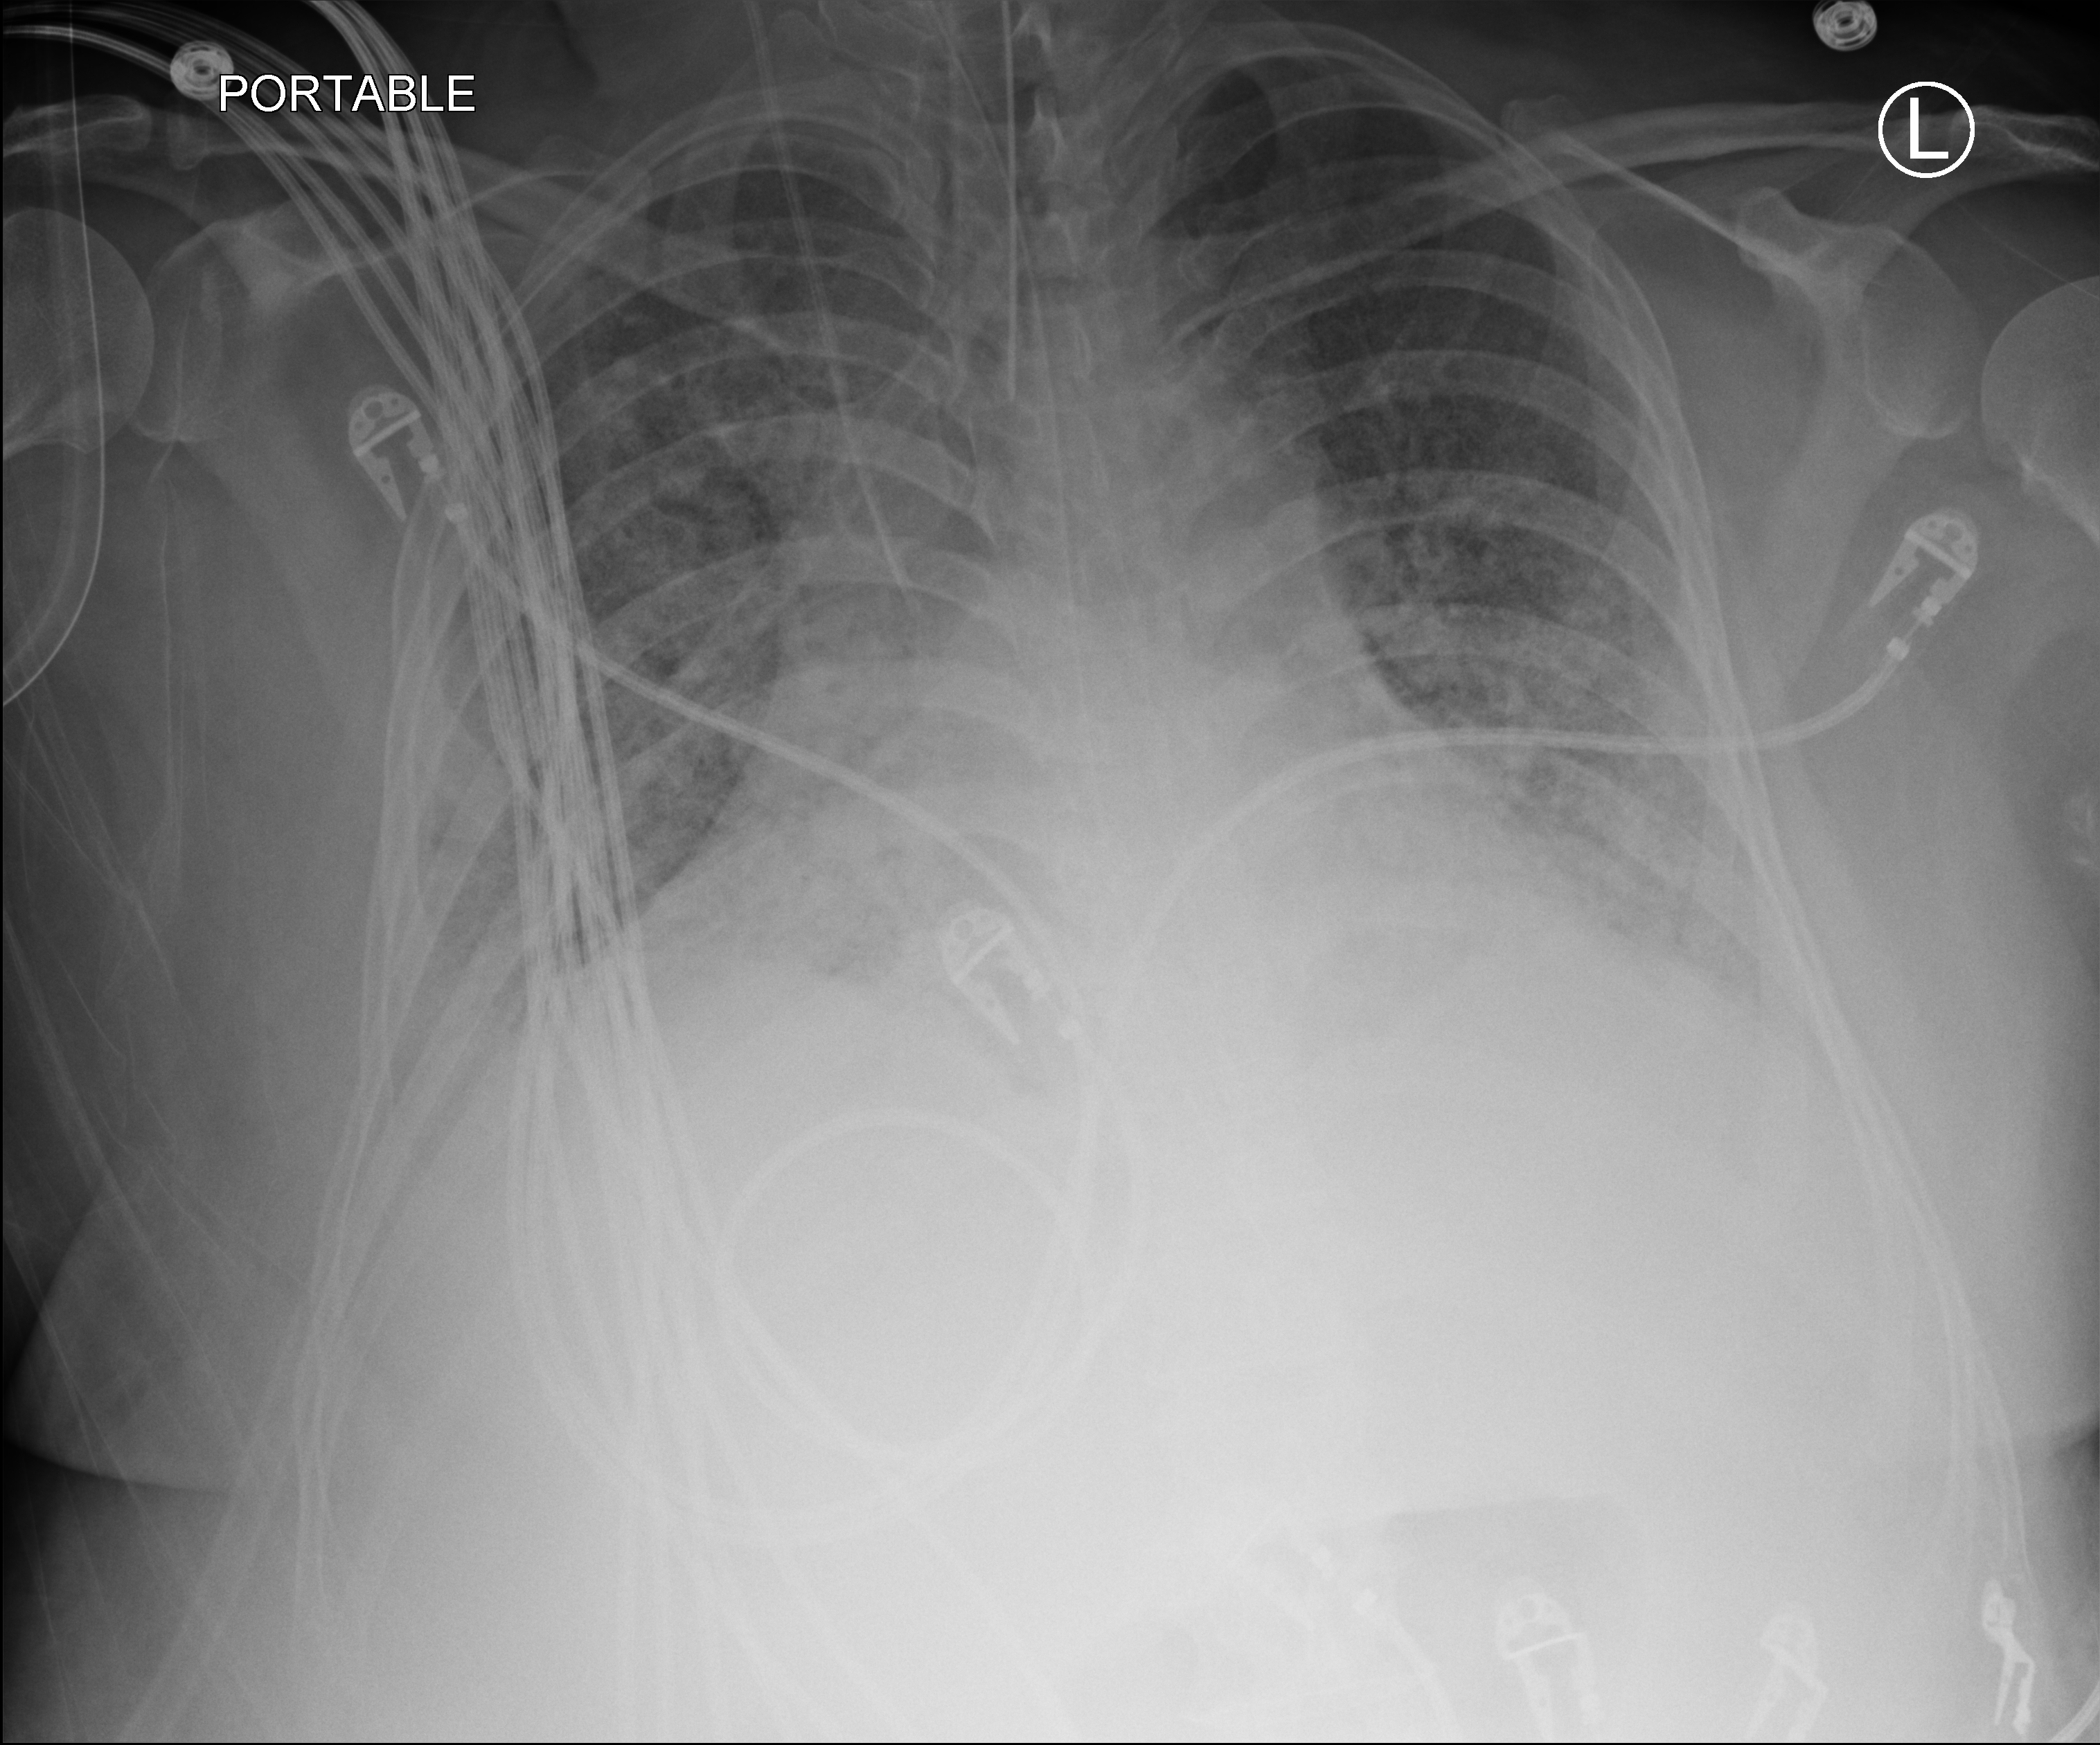
Chest X-ray (portable); anteroposterior (AP) projection. Patient hospitalised with COVID-19, aged 18–59 years.
Hospital-stay facts (about this admission, not read from this image; timing relative to this image not recorded):
- length of hospital stay: 48 days
- mechanically ventilated during this hospital stay: yes